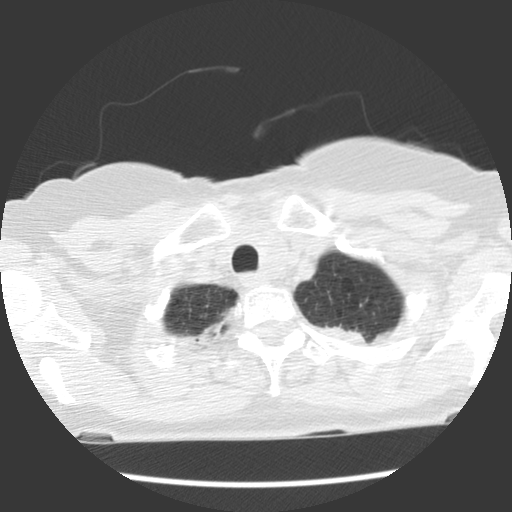
Low-dose screening chest CT, one axial slice; slice 106 of 120 in the series (ordered by position); 140 kVp; lung window (W 1500 / L -600 HU); 2.5 mm slice thickness; 512 × 512 image matrix, field of view 300 × 300 mm.
Structures marked on this image (outlined manually by an expert reader):
- lesion 1 (tumor, upper lobe of left lung): bounding box (x1, y1, x2, y2) in pixels: (327, 326, 389, 343)